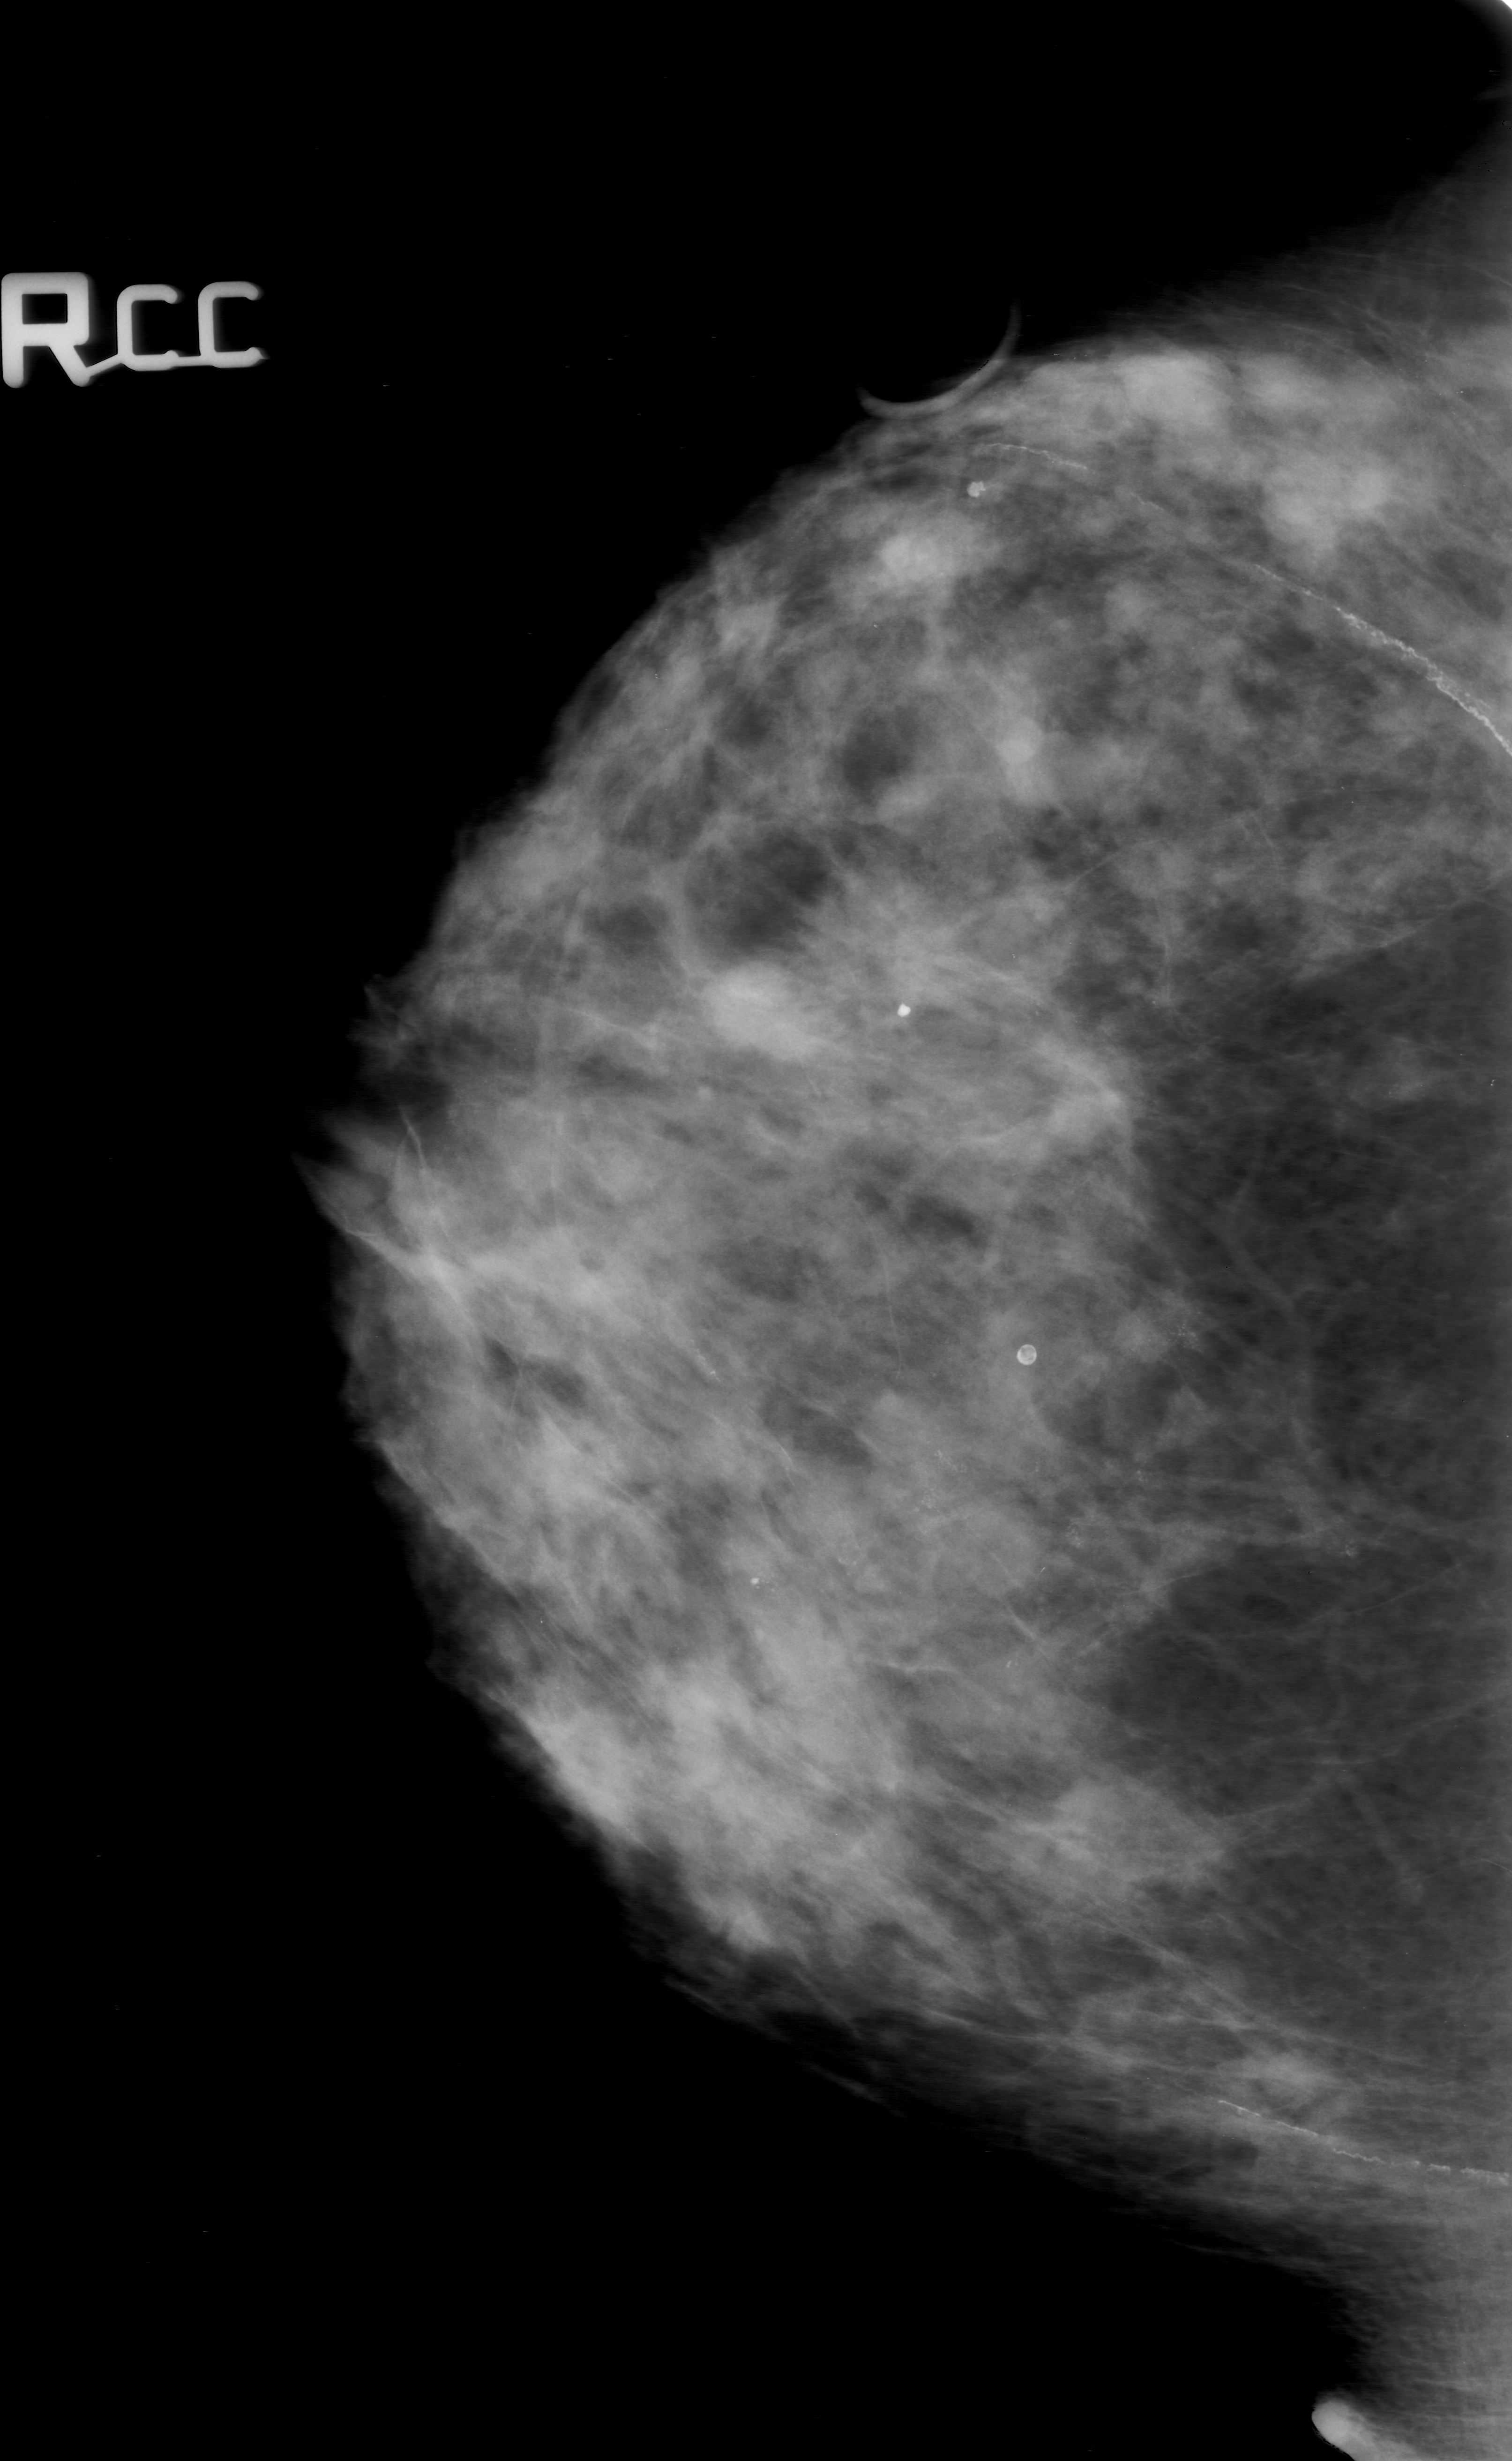
Mammogram (digitized film). Right breast. CC view. Breast composition: heterogeneously dense (BI-RADS density category 3 of 4). 1512 × 2461 image matrix.
Expert-marked regions of interest on this film, with their recorded descriptors:
- calcifications, morphology amorphous, distribution segmental; BI-RADS assessment category 5; subtlety rating 3 on a 1 (subtle) to 5 (obvious) scale; pathology (as recorded): malignant: bounding box <760,1234,1316,1714> (left, top, right, bottom; pixels)